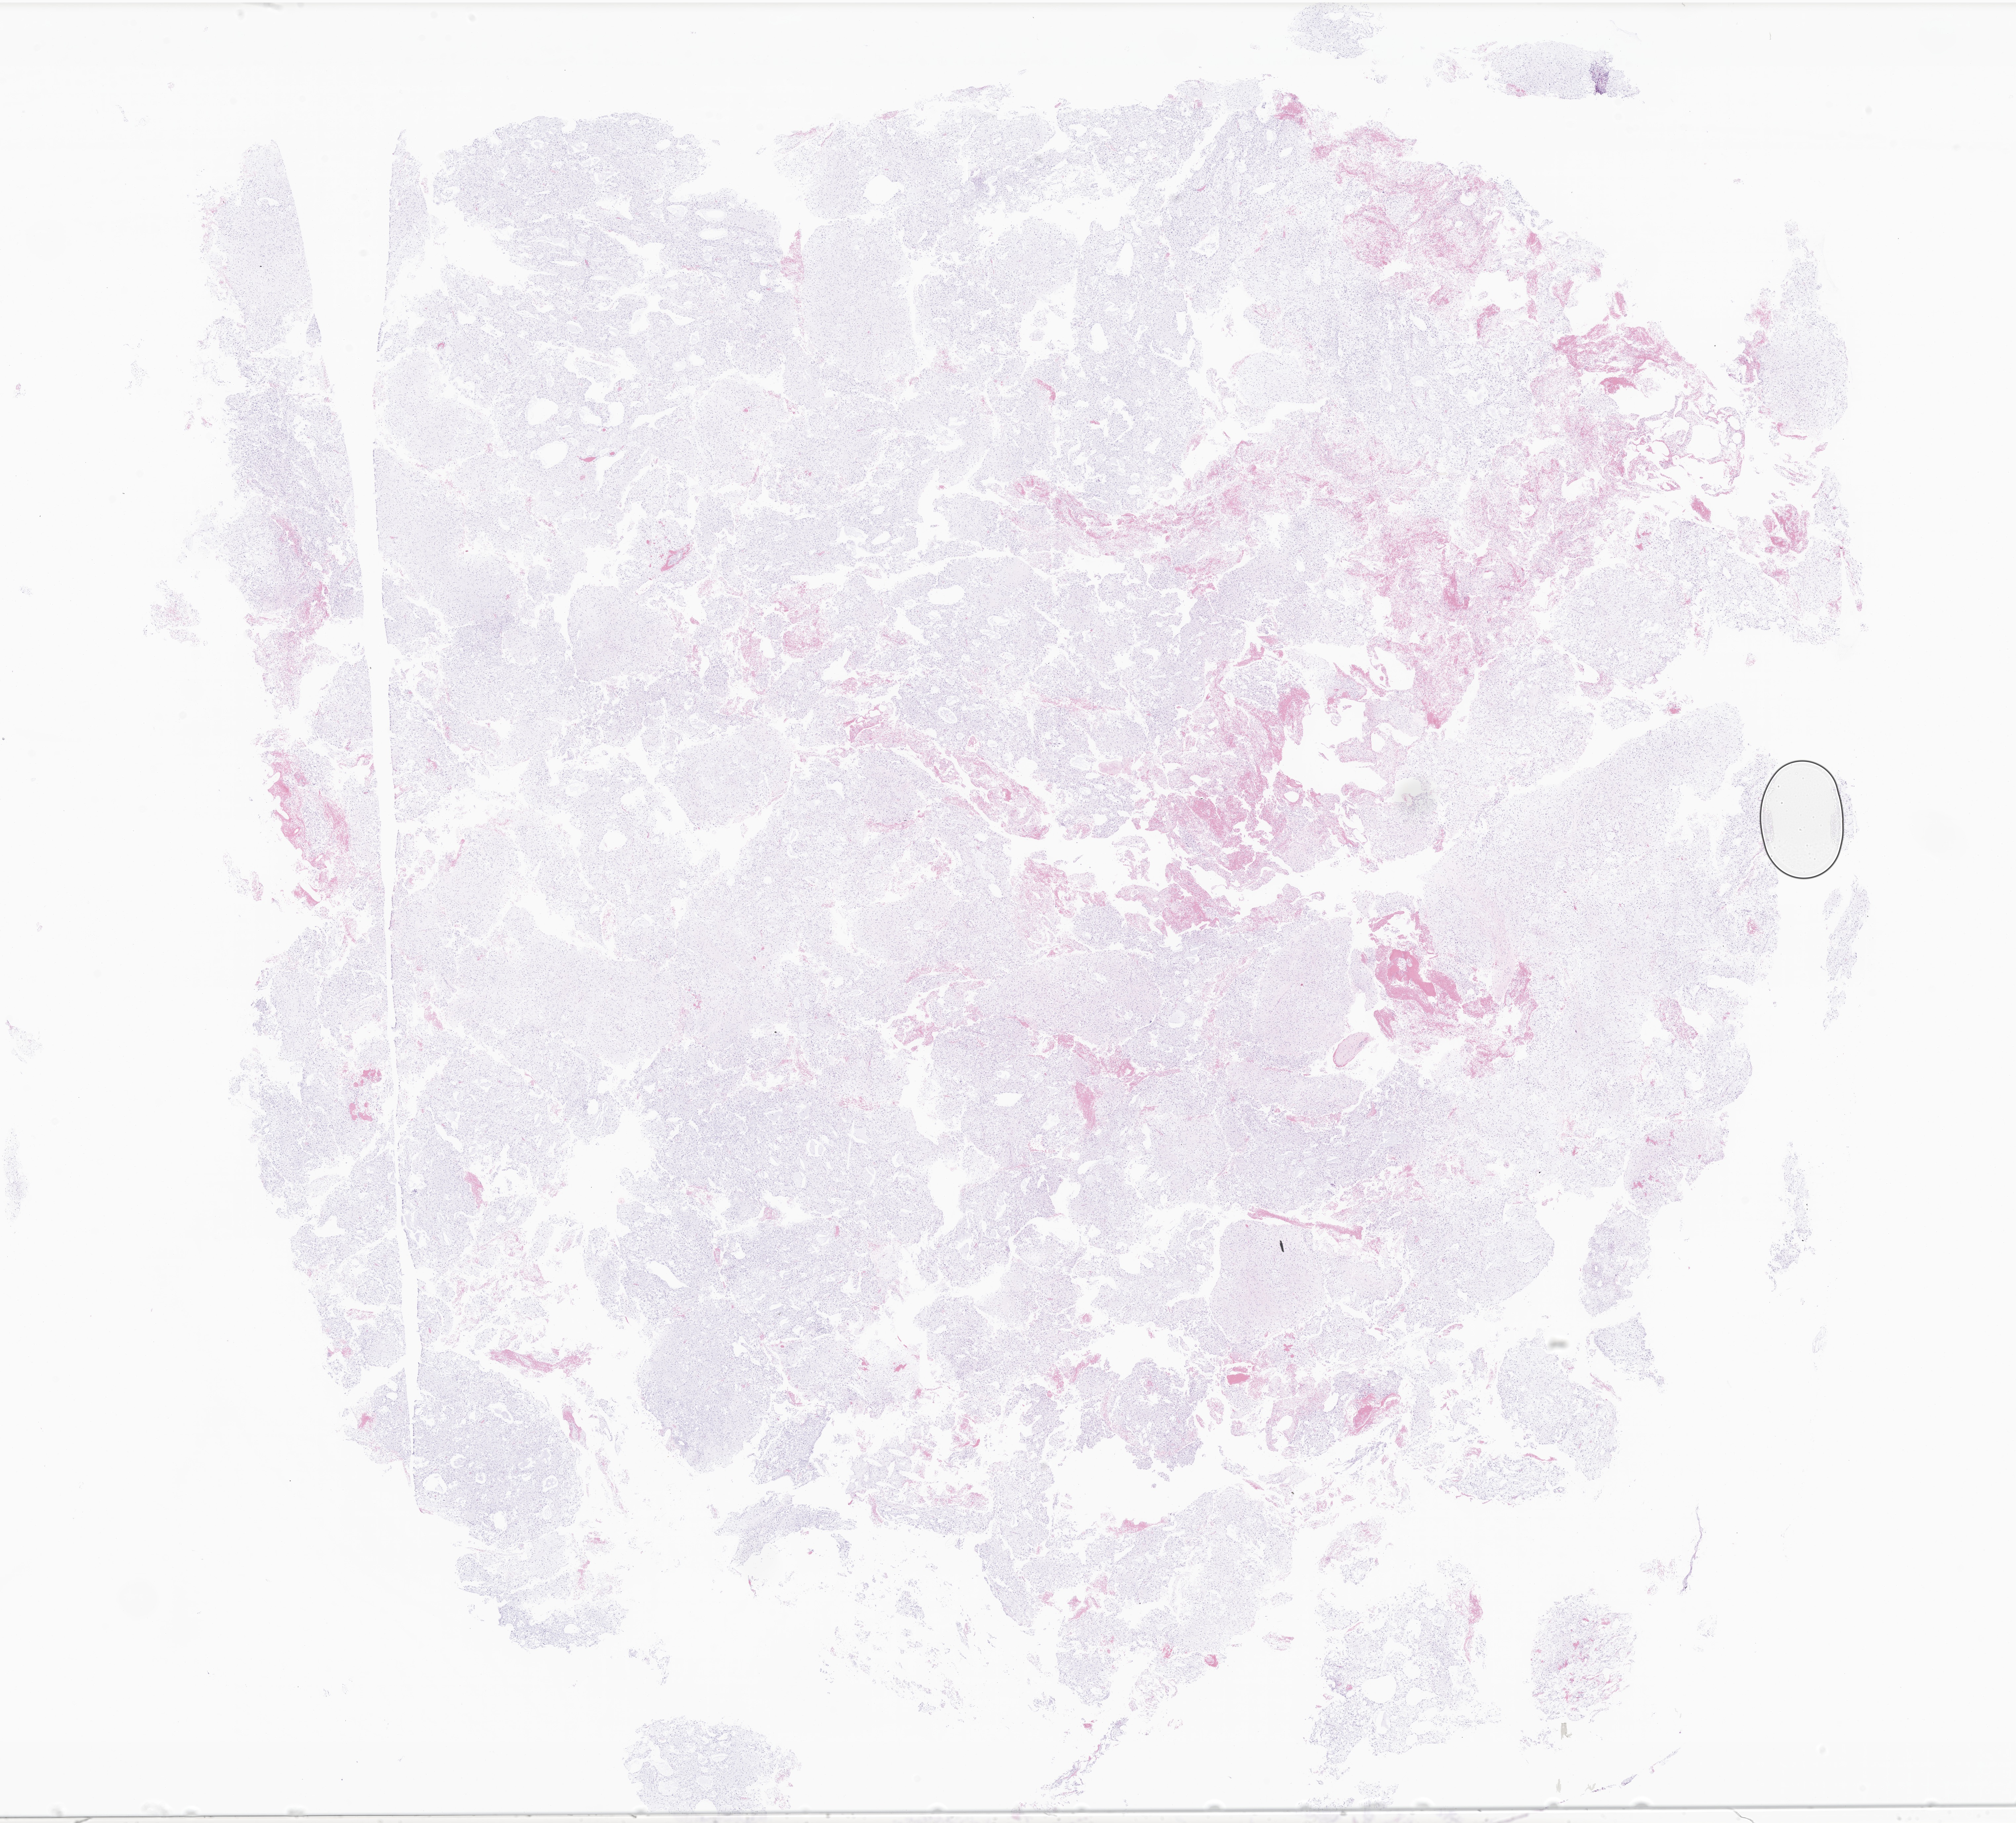
Whole-slide image, H&E stain of tumor tissue from the brain, low-resolution overview of the scanned area, about 25.7 x 23.2 mm. FFPE section. Patient female; age 194 months.
- diagnosis (ICD-O-3 morphology term): Pilocytic astrocytoma